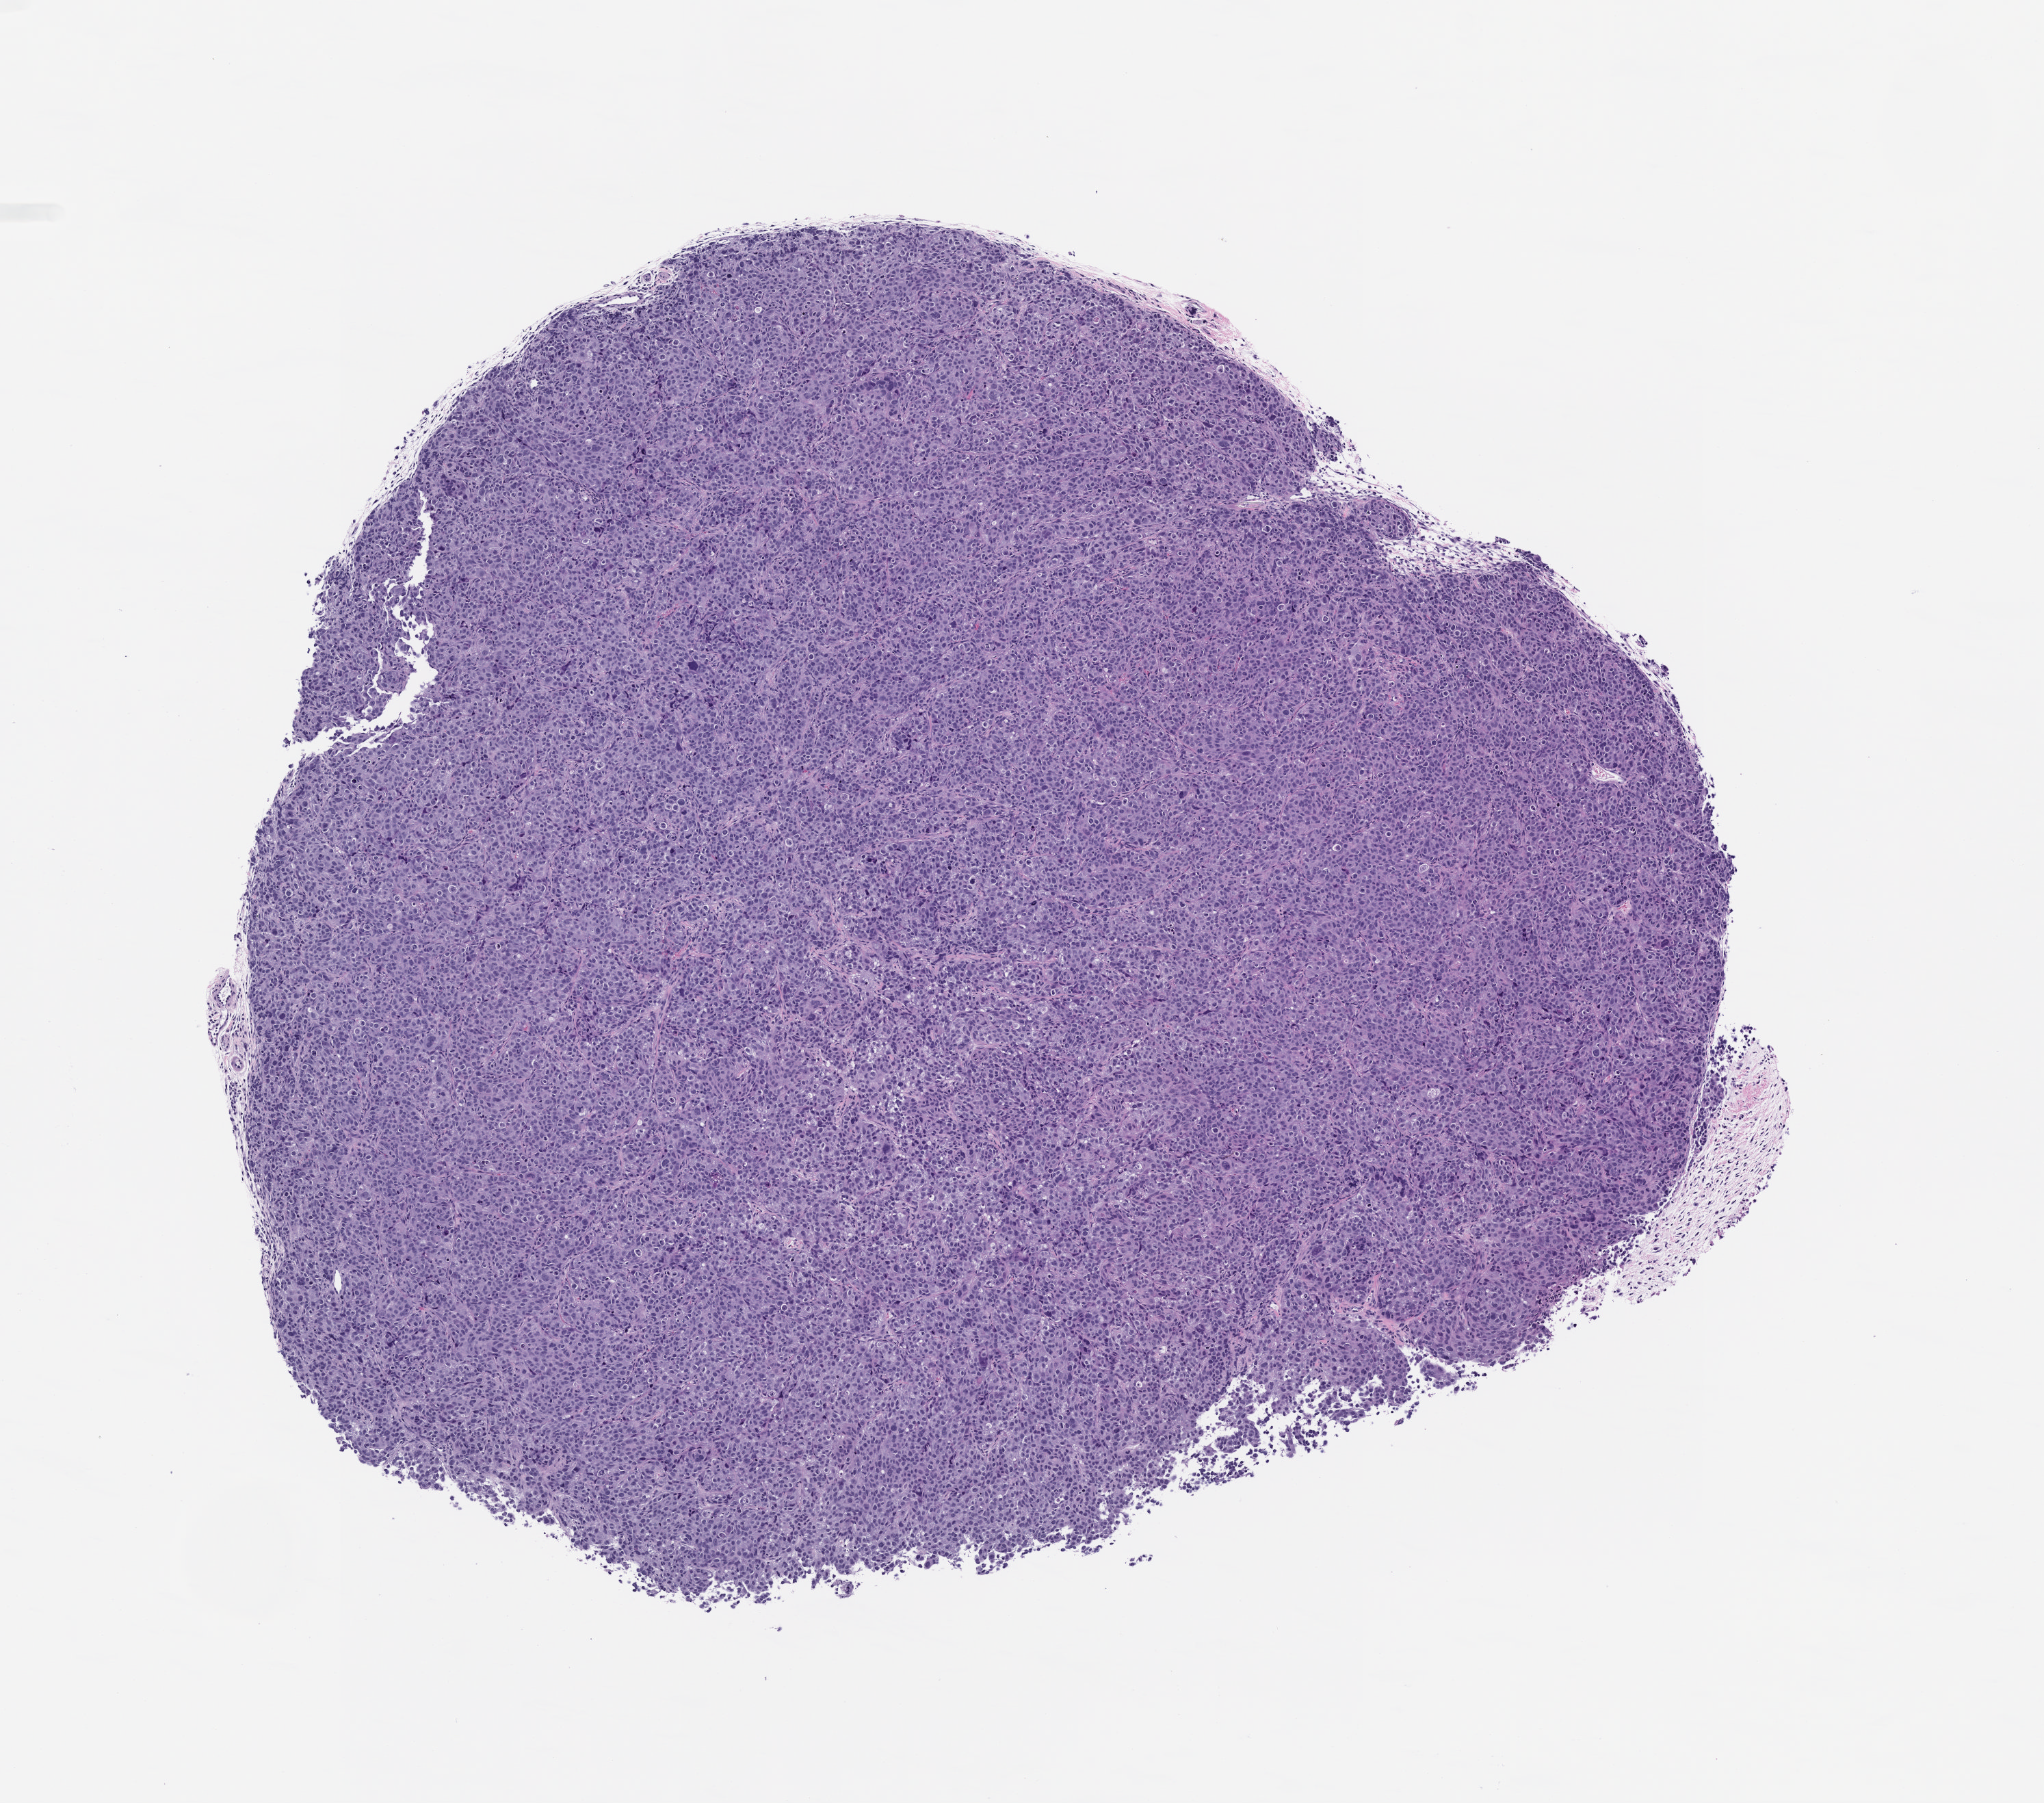
Whole-slide image, hematoxylin and eosin (H&E): patient-derived xenograft (human tumor grown in a mouse), passage 2 — shown as a low-resolution overview of the whole scanned area (about 6.0 x 5.3 mm); formalin-fixed paraffin-embedded section; tumor site category: lung.
Originating patient diagnosis: Lung Squamous Cell Carcinoma.